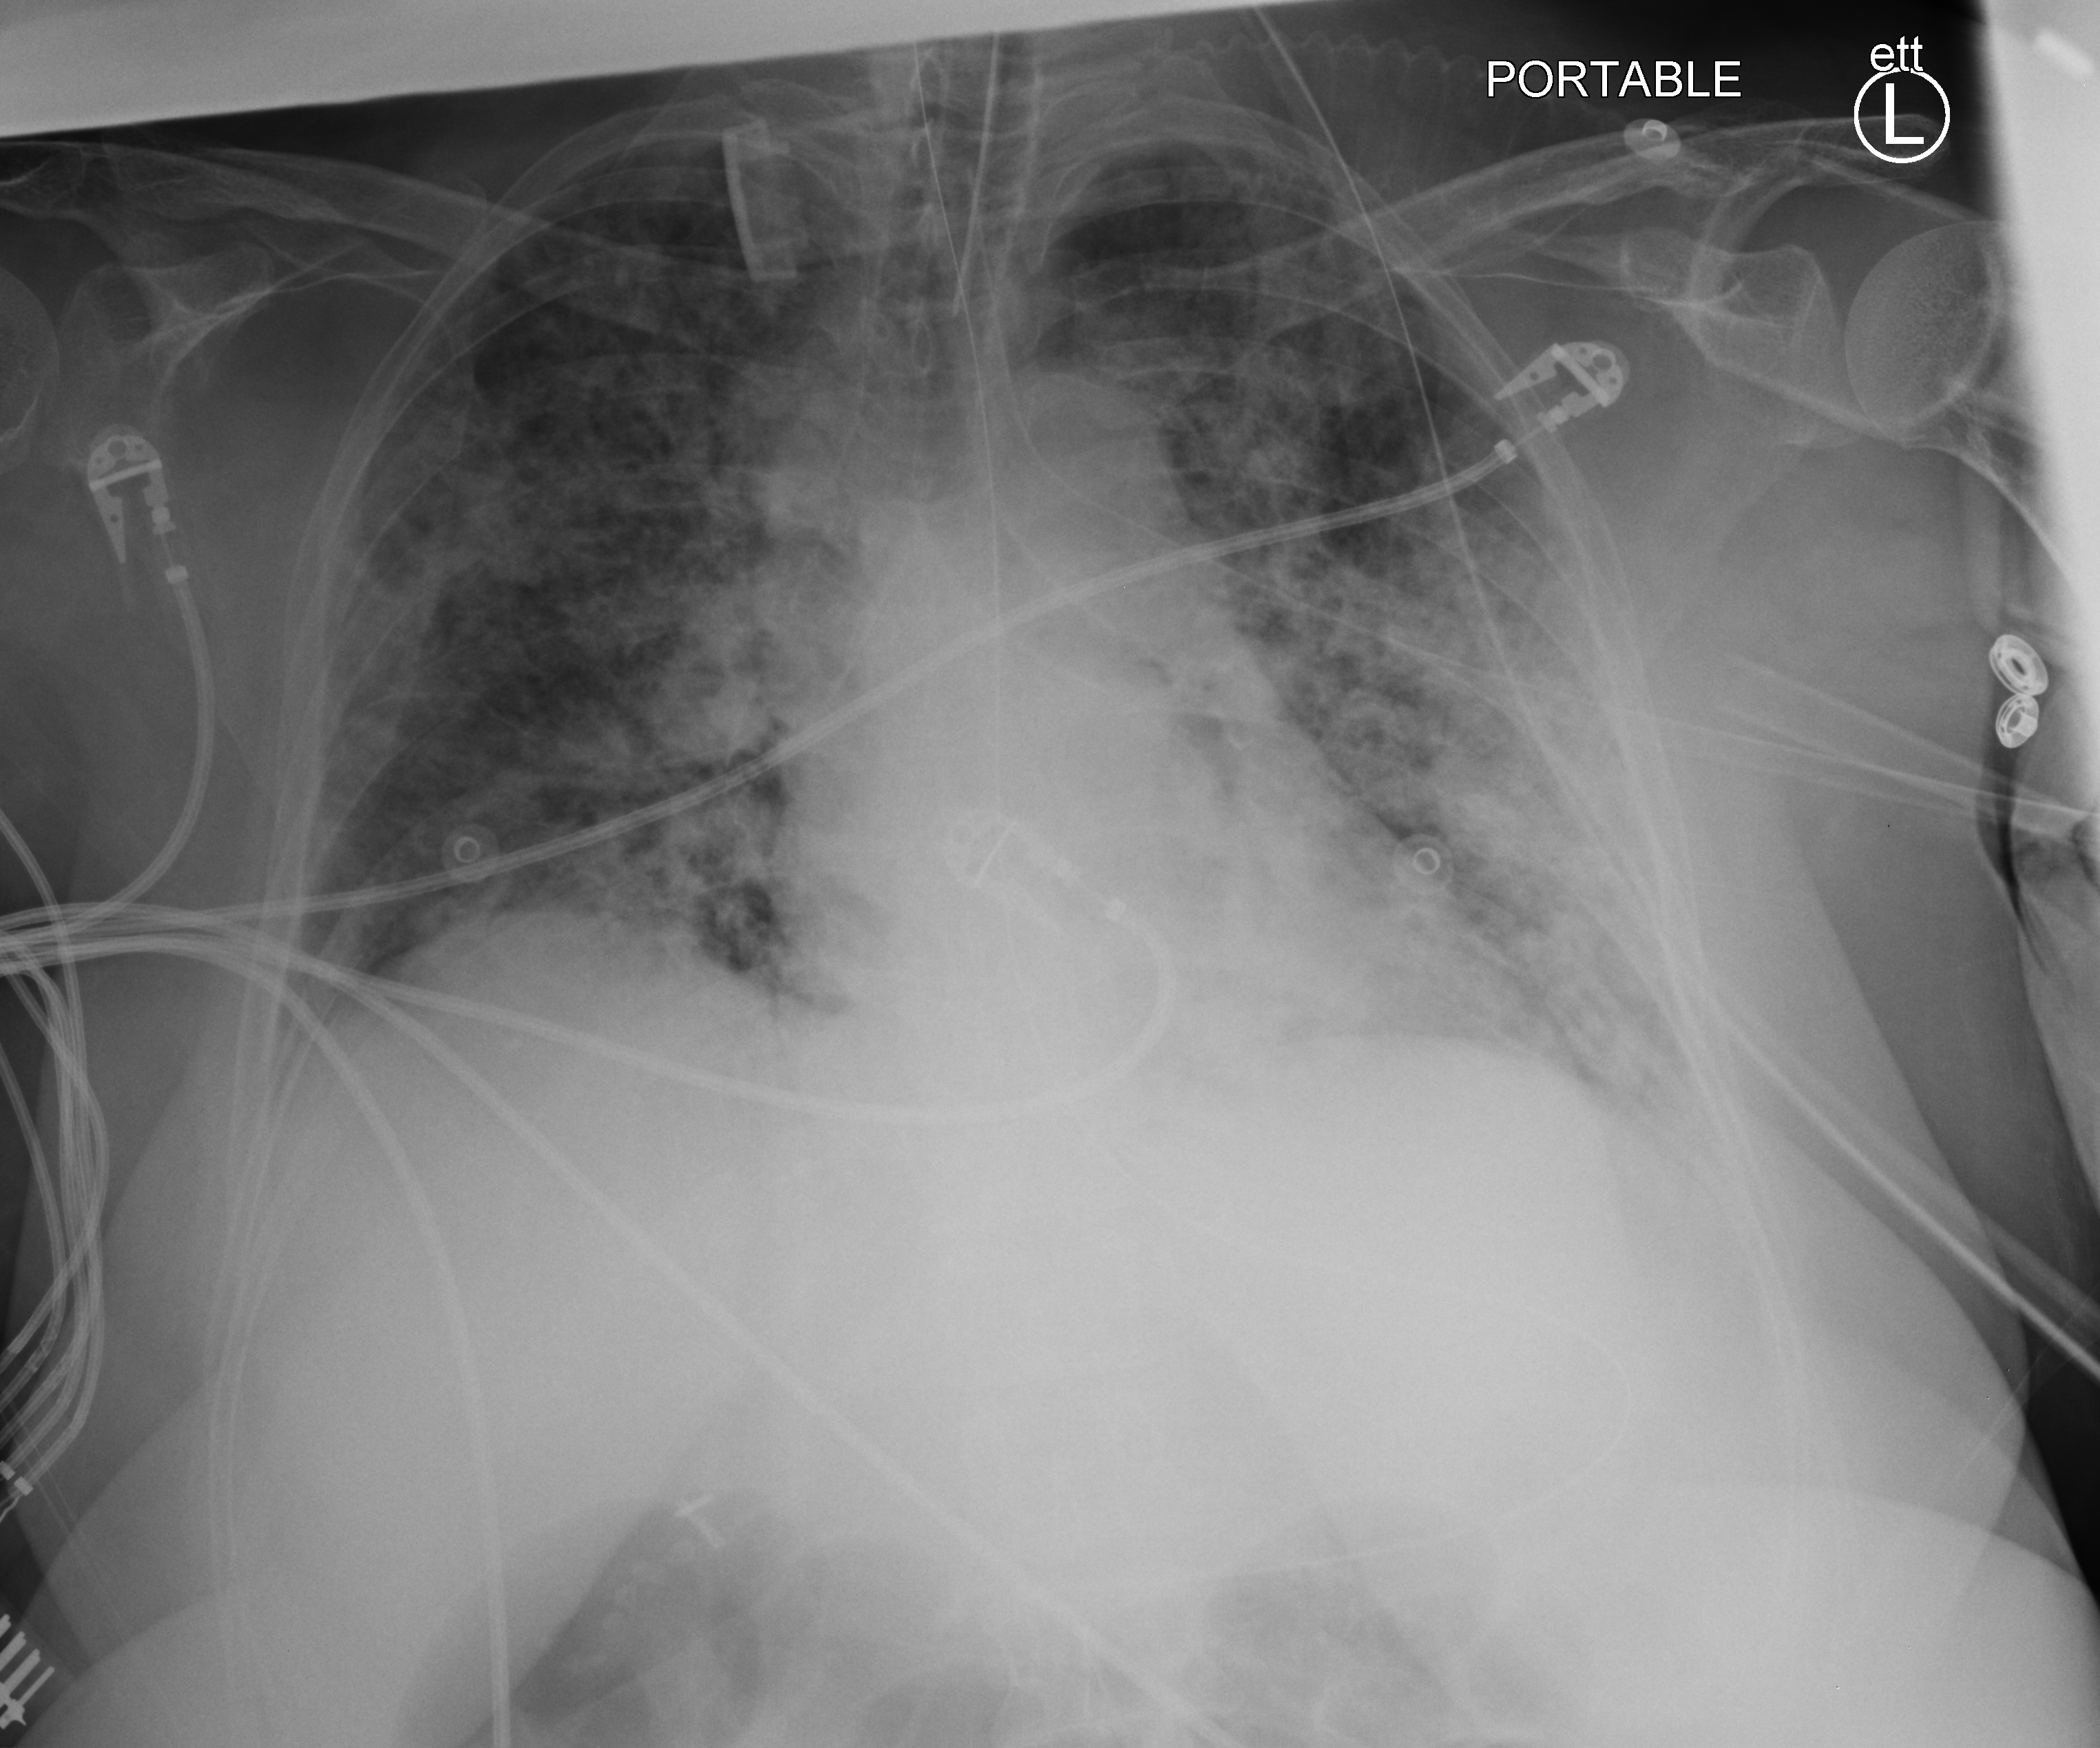
Chest X-ray (portable), anteroposterior (AP) projection. Female patient hospitalised with COVID-19, age 18–59 years.
Hospital-stay facts (about this admission, not read from this image; timing relative to this image not recorded):
- other chronic lung disease (admission record): no
- length of hospital stay: 22 days